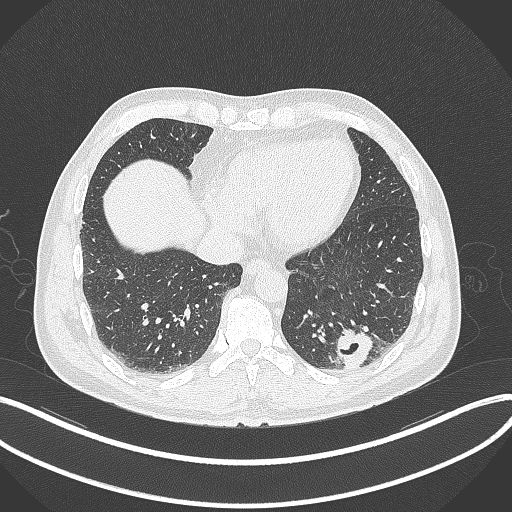
Chest CT, one axial slice; slice 78 of 300 in the series (ordered by position); reconstruction kernel B70f; 120 kVp; lung window (W 1500 / L -600 HU); 1 mm slice thickness; 512 × 512 image matrix, field of view 400 × 400 mm. Male patient, age 54 years. Case-level facts recorded for this patient, not image findings: clinical TNM (as recorded): T1c N0 M1; histopathological grade: G3.
Structures marked on this image (rectangle marked by the reading radiologist):
- lung tumour (recorded histology: adenocarcinoma): bounding box <334,322,373,369> (left, top, right, bottom; pixels)